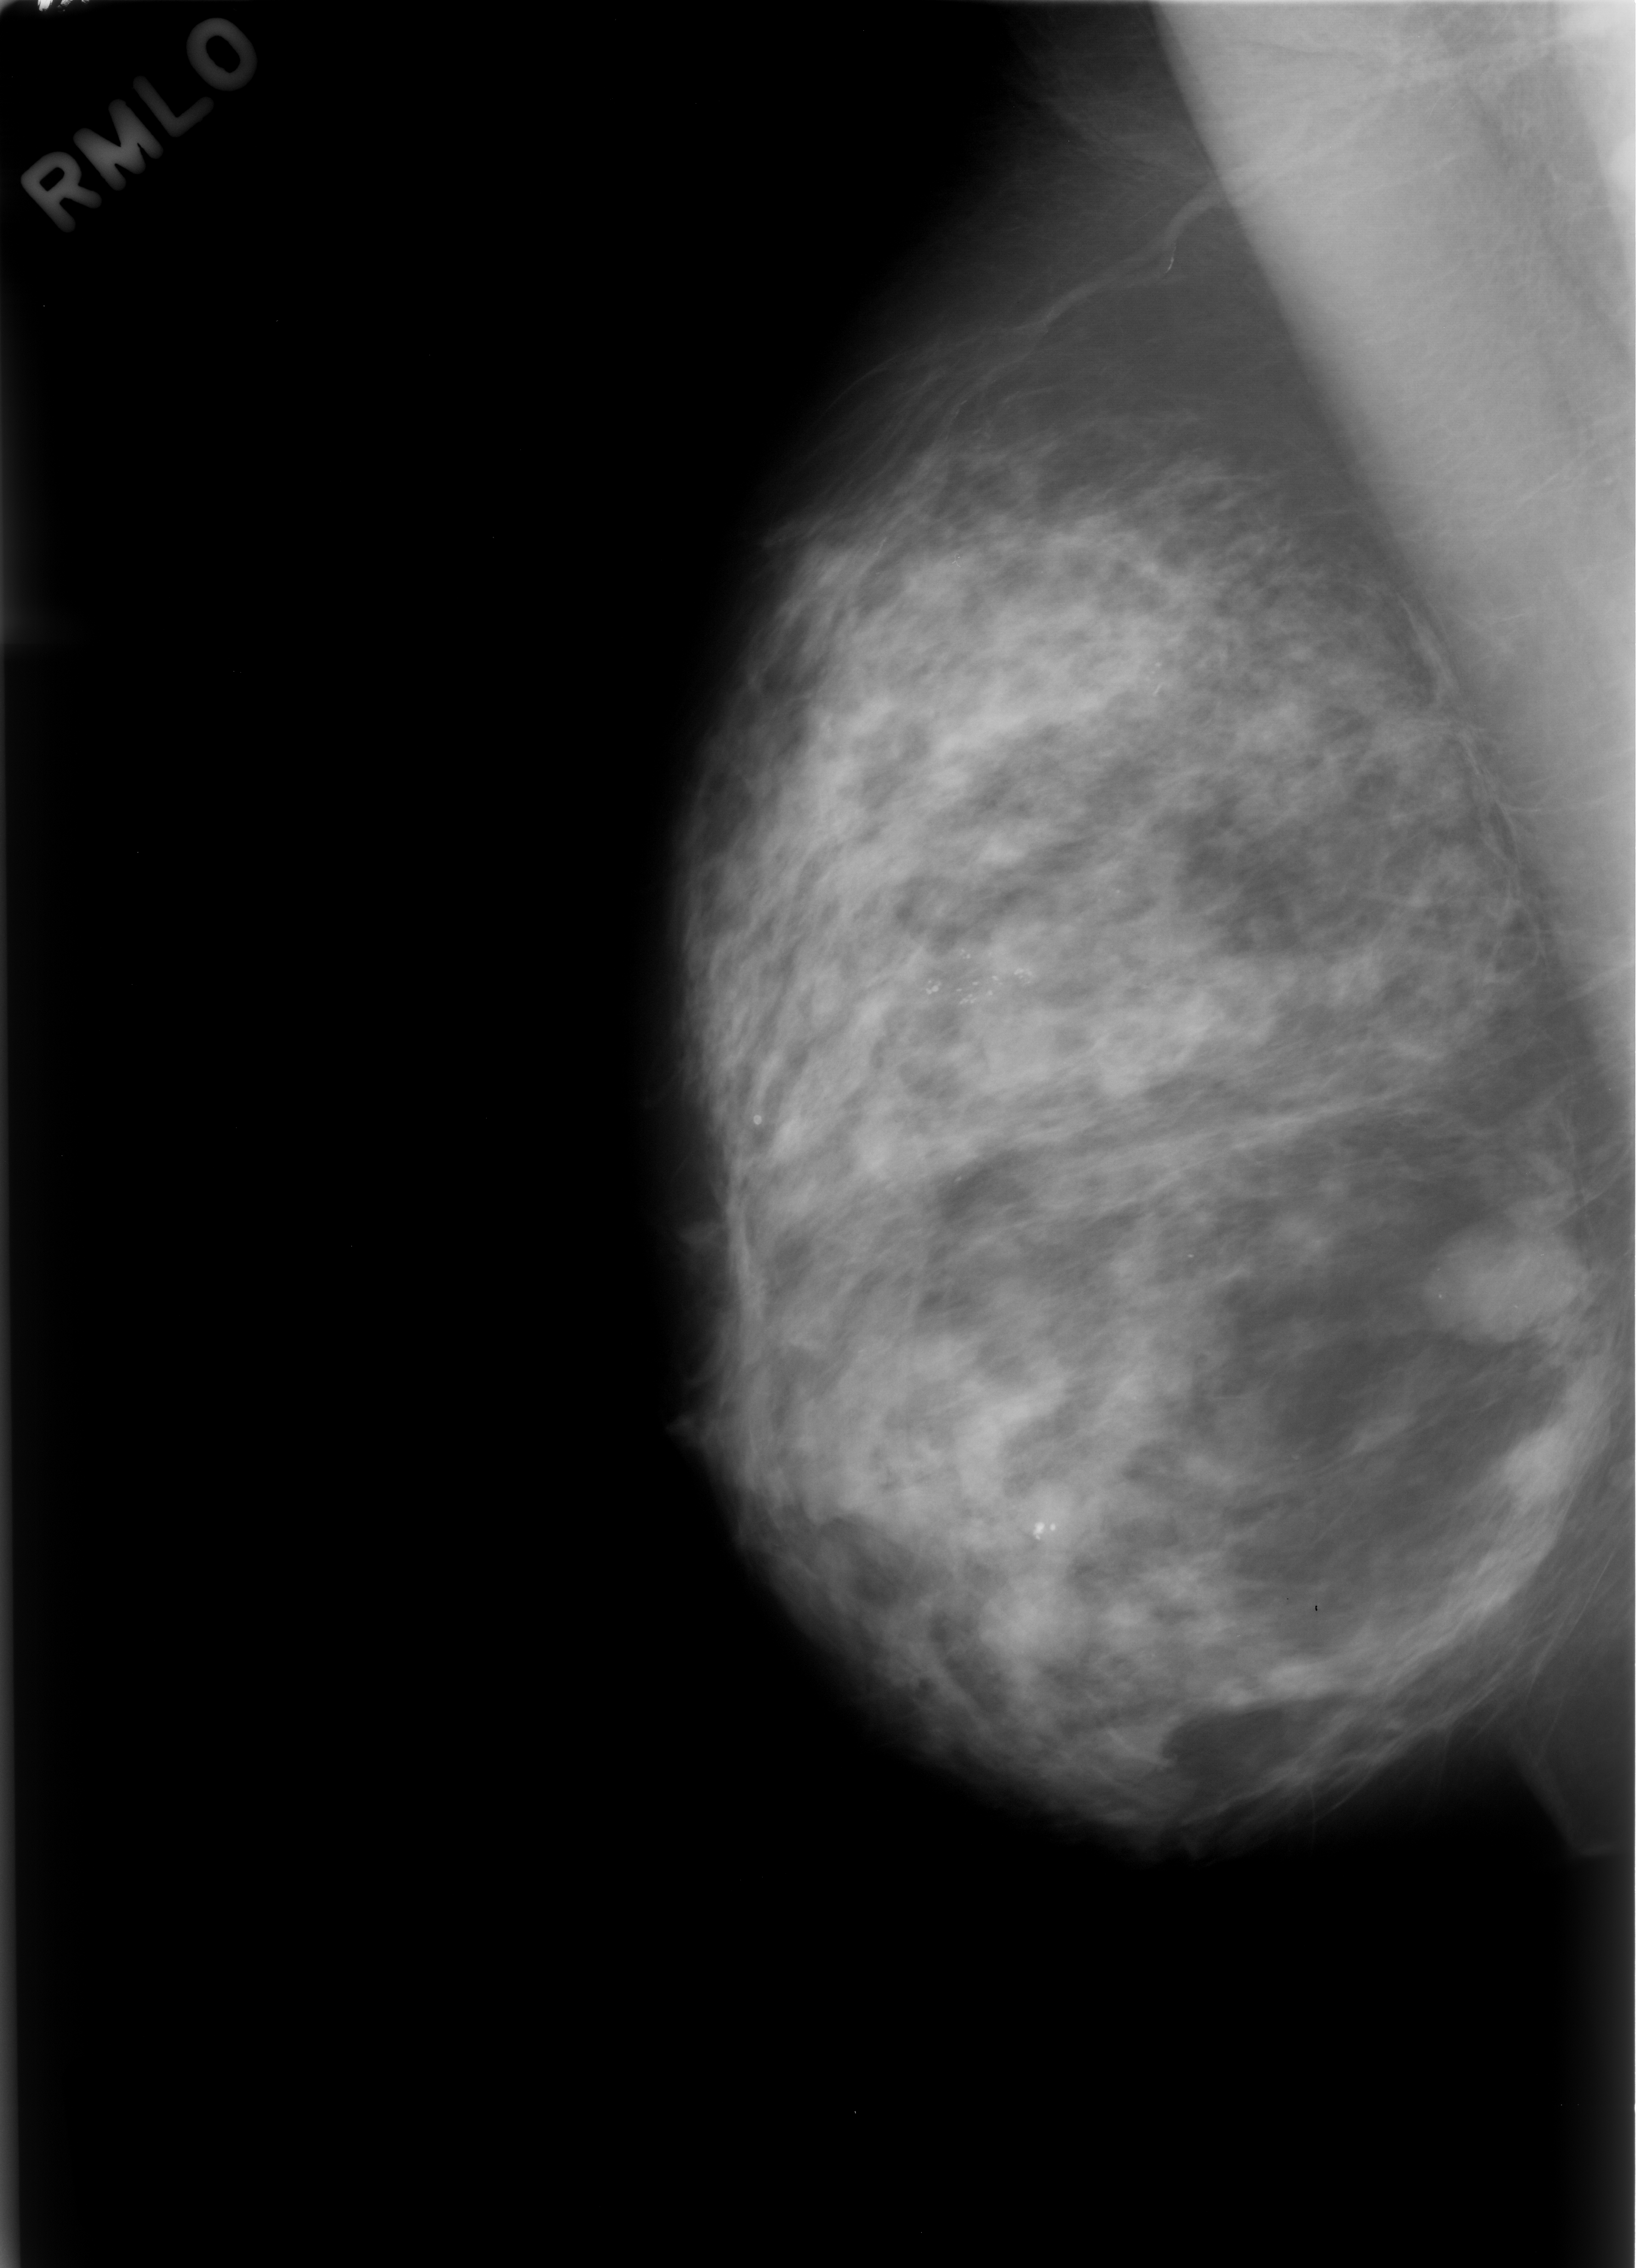
Scanned film-screen mammogram; right breast; MLO view; breast composition: heterogeneously dense (BI-RADS density category 3 of 4); 1640 × 2268 image matrix.
Expert-marked regions of interest on this image (one box per marked abnormality):
- mass, shape lobulated, margins circumscribed; BI-RADS assessment category 3; subtlety rating 5 on a 1 (subtle) to 5 (obvious) scale; pathology result (as recorded, not read from the image): benign: box from (x=1442, y=1222) to (x=1571, y=1332) px